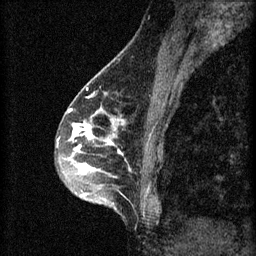
Breast MRI (dynamic contrast-enhanced), one sagittal slice; position 26 of 60 along the scan axis; 3 images stored at this slice position (order not interpretable as contrast timing); 1.5 T; TE 4.2 ms, TR 8.2 ms; 2 mm slice thickness; 256 × 256 image matrix, field of view 180 × 180 mm. Patient: female, 45 years.
Structures marked on this image (semi-automatically segmented with operator editing):
- analysis volume of interest (the breast-tissue region the enhancement analysis was run in; not a lesion): bounding box (x1, y1, x2, y2) in pixels: (56, 104, 159, 217)
- tumour enhancement mask (voxels above the 70 % enhancement threshold inside the analysis volume of interest): (58, 108, 123, 197)